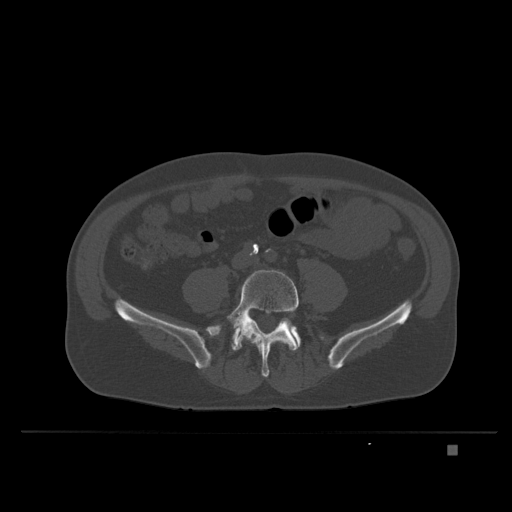
CT including the spine, one axial slice; slice 57 of 435 in the series (ordered by position); bone window (W 1800 / L 400 HU); 1.5 mm slice thickness; 512 × 512 image matrix, field of view 434 × 434 mm. Male patient, age 73 years. From the clinical record (not read from this slice): primary cancer: skin.
Structures marked on this image (semi-automatic segmentation, software-assisted and operator-edited):
- L5 vertebra: bounding box (x1, y1, x2, y2) in pixels: (226, 269, 299, 378)